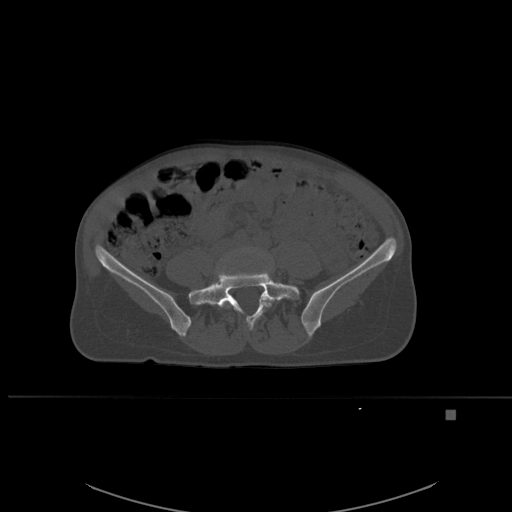
CT including the spine, one axial slice. Slice 177 of 537 in the series (ordered by position). Bone window (W 1800 / L 400 HU). 512 × 512 image matrix. Patient: female, 45 years. Case-level facts recorded for this patient, not image findings: primary cancer: lung.
Structures marked on this image (semi-automatically segmented with operator editing):
- L4 vertebra: bounding box (x1, y1, x2, y2) in pixels: (221, 248, 268, 306)
- L5 vertebra: (196, 266, 300, 331)